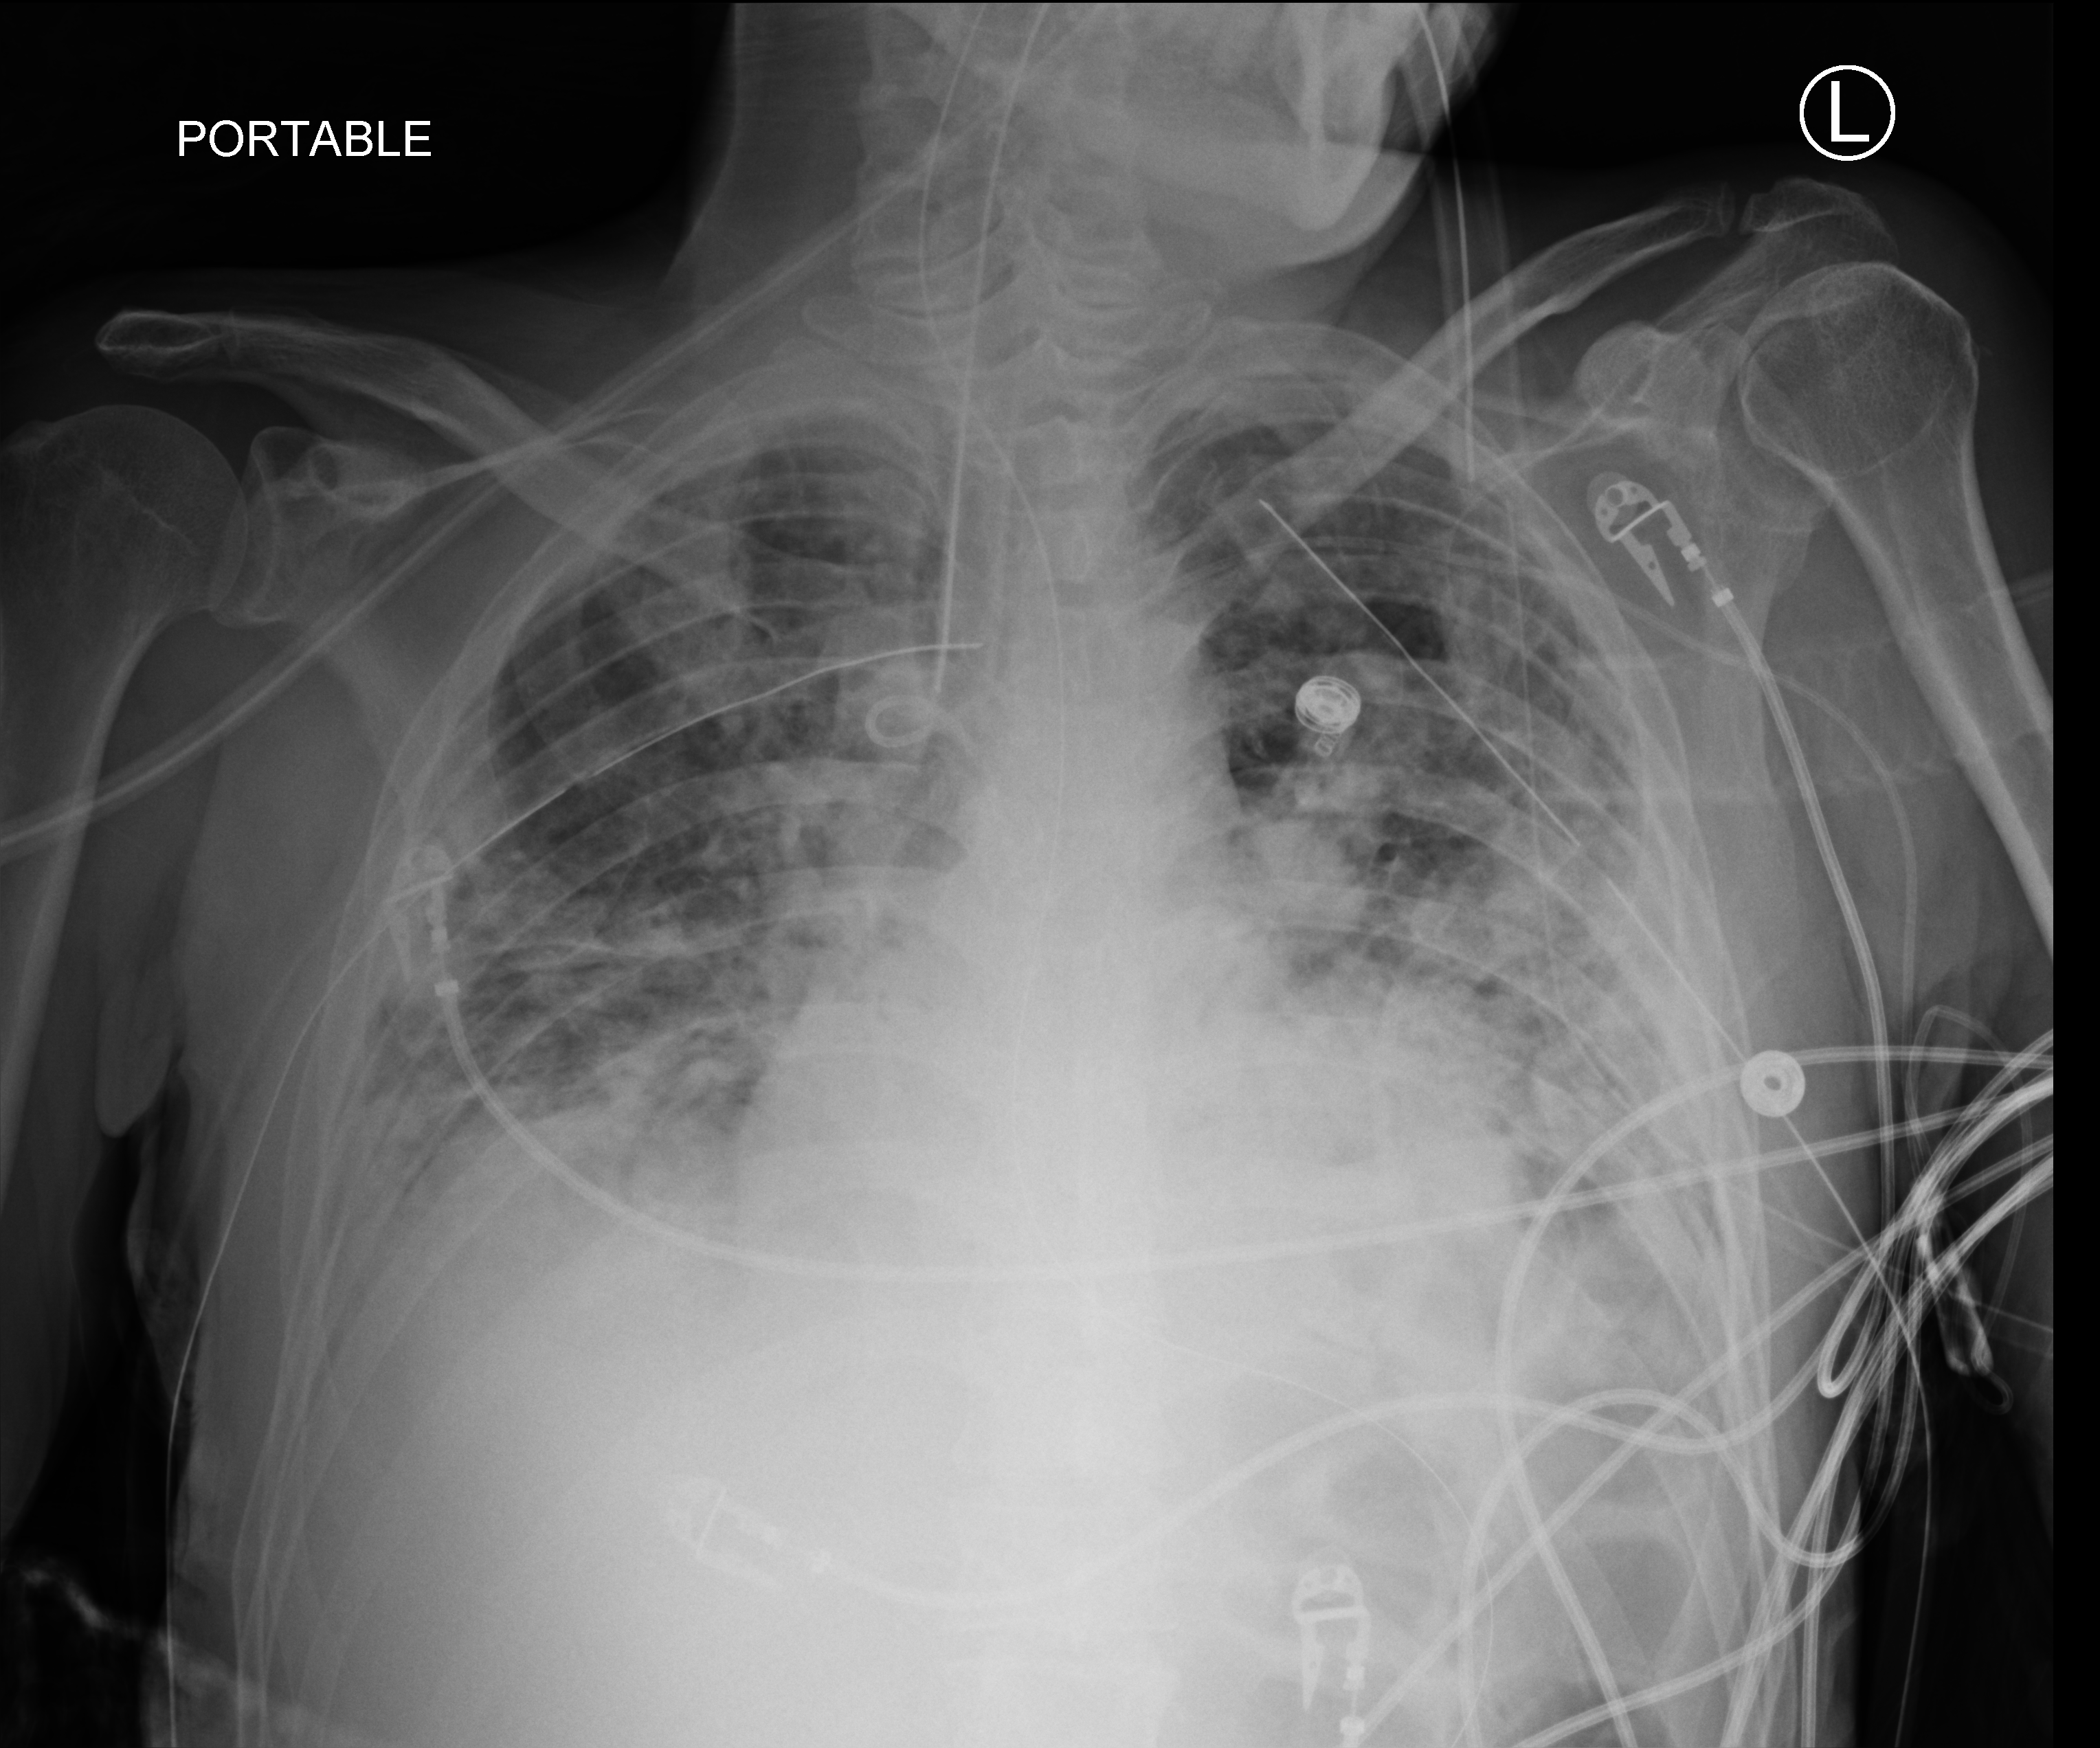
Bedside chest radiograph (computed radiography), anteroposterior (AP) projection. Male patient hospitalised with COVID-19, age 18–59 years.
Hospital-stay facts (about this admission, not read from this image; timing relative to this image not recorded): length of hospital stay: 96 days; hypertension (admission record): yes; smoking status (admission record): never.